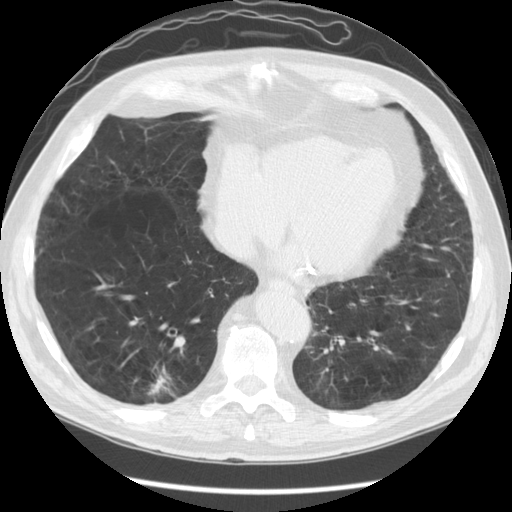
Axial slice from a low-dose chest CT screening exam. Baseline screening round. Lung window (W 1500 / L -600 HU). 2.5 mm slice thickness. Standard (soft-tissue) reconstruction kernel (STANDARD). 120 kVp. Slice 96 of 141 in the series. 512 × 512 image matrix. Male, age 67 years at enrolment. Former smoker at enrolment.
- Expert-annotated lung lesion, box from (x=120, y=356) to (x=187, y=417) px.
- The screening reader recorded 2 non-calcified nodules or masses ≥4 mm on this exam (right lower lobe, right lower lobe); which of them this box marks is not recorded.